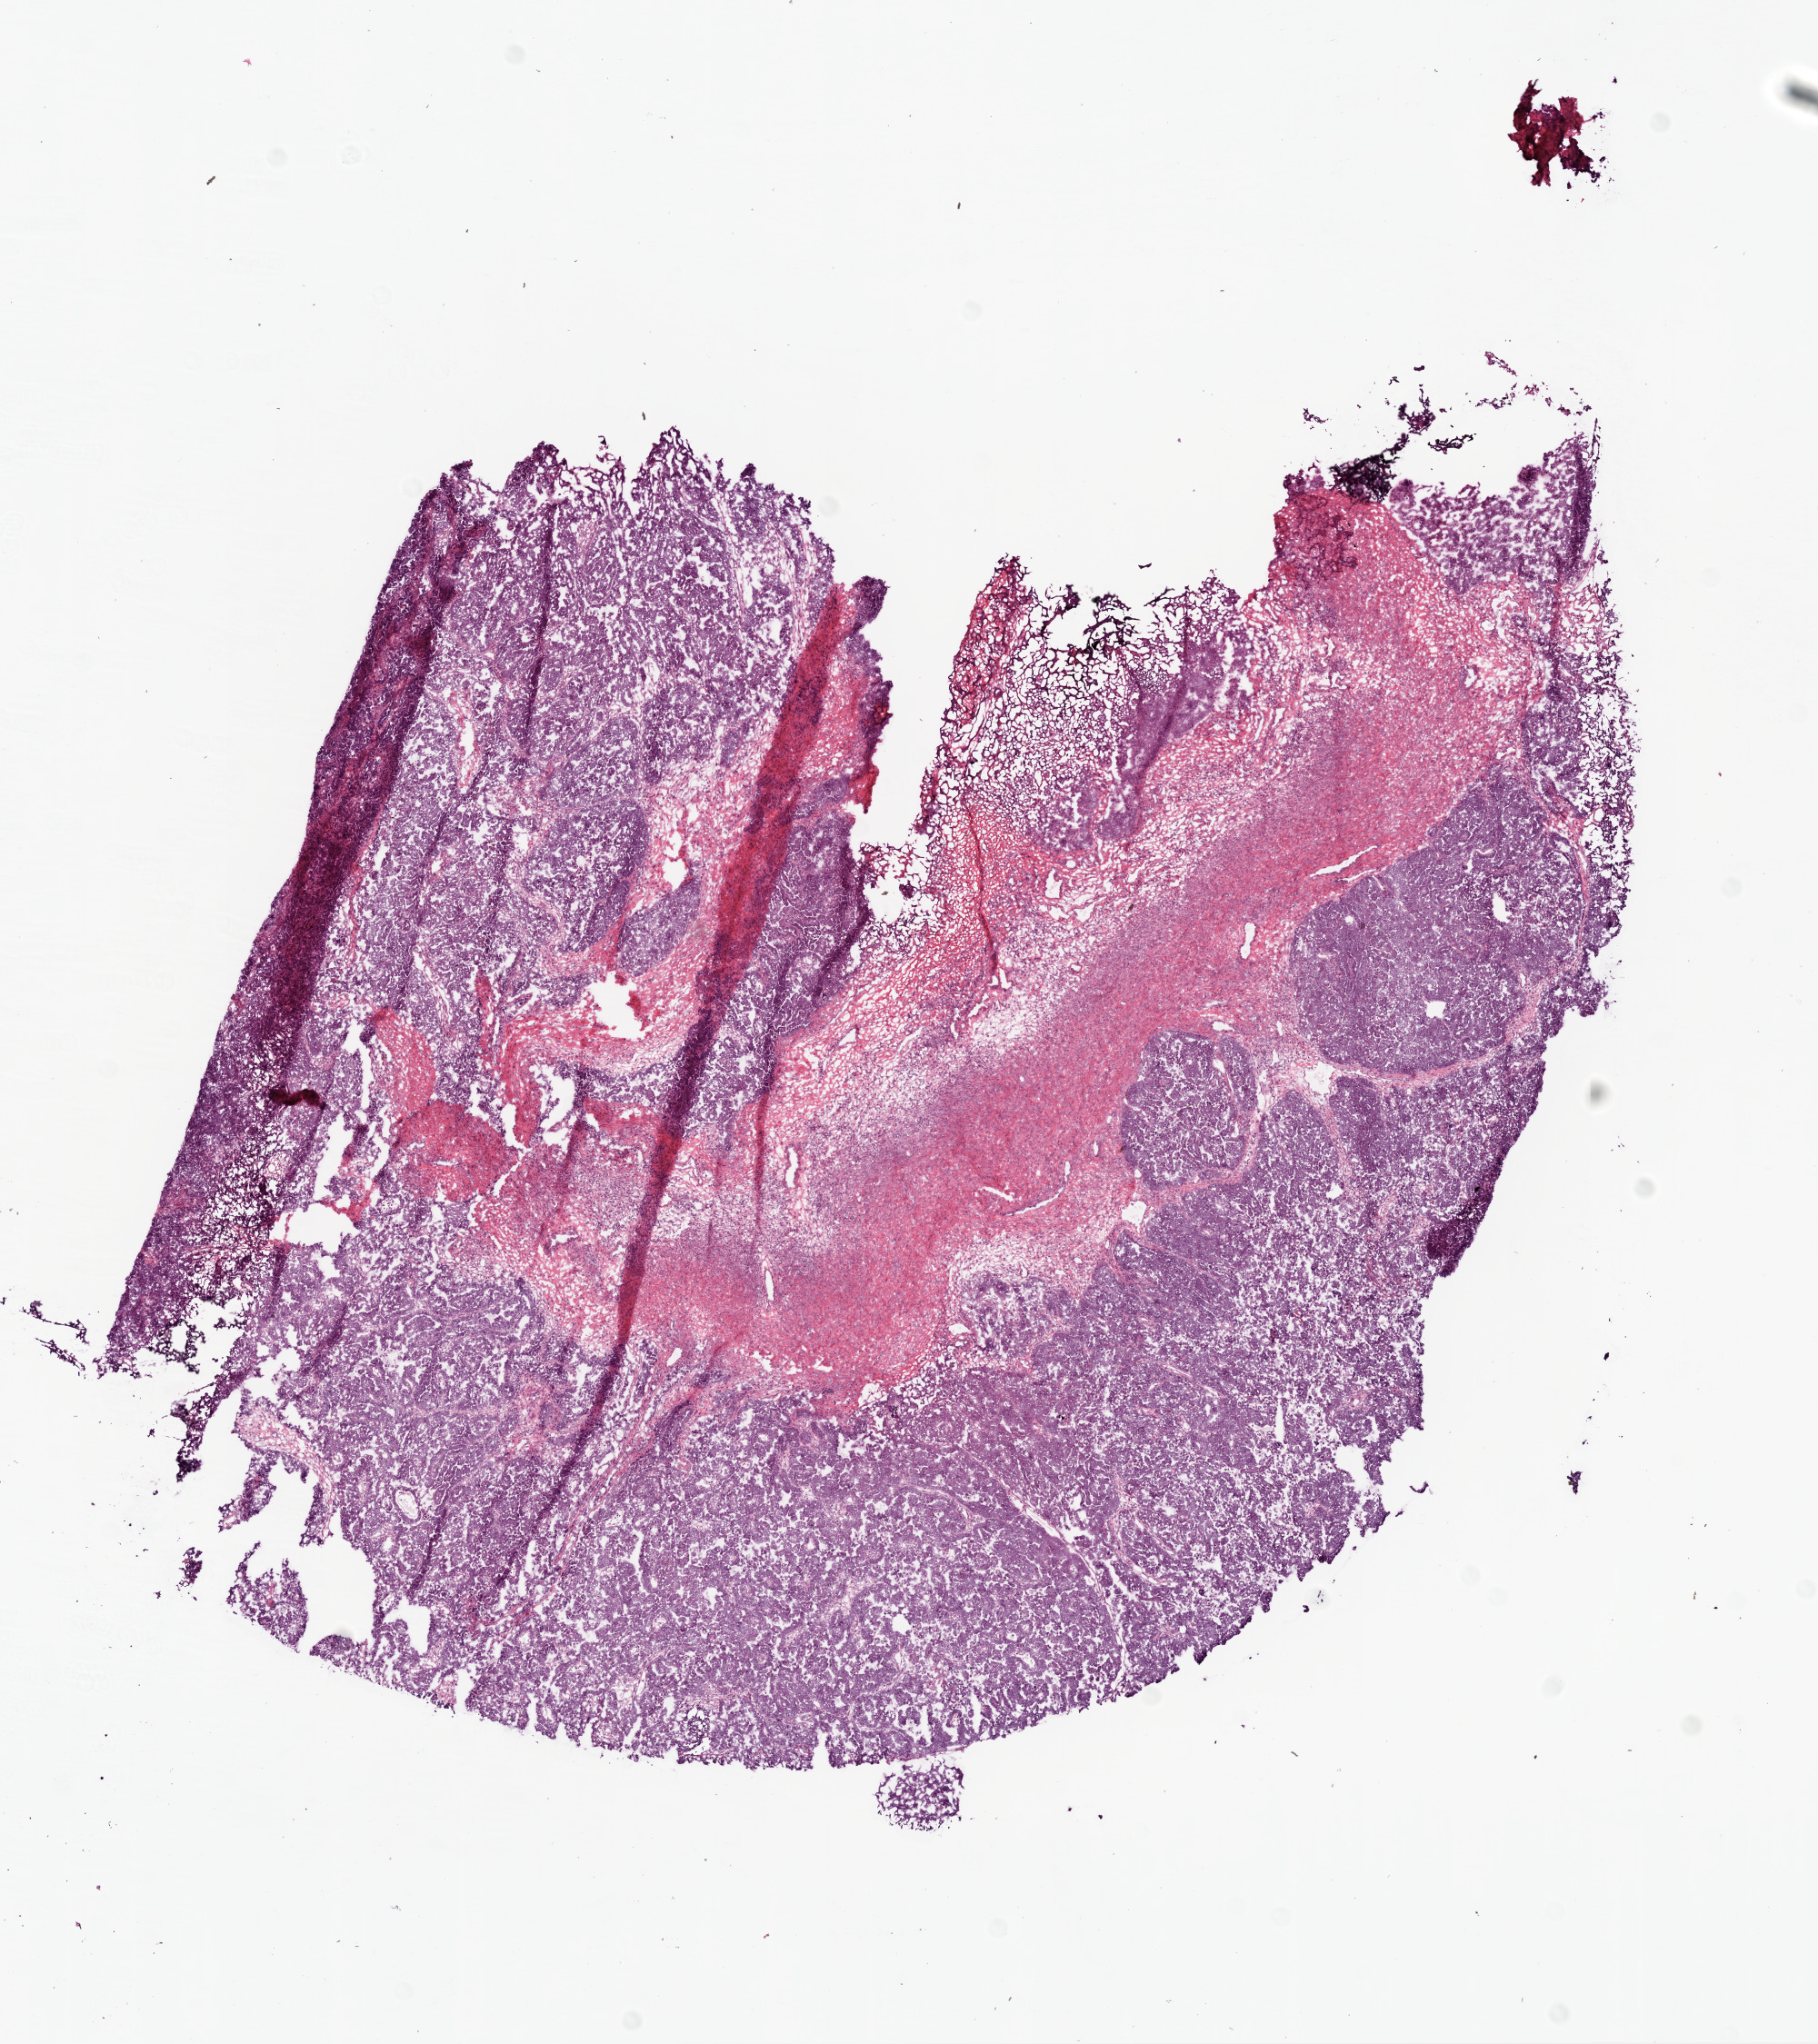
Digitized Hematoxylin and eosin (H&E) stained tissue section (whole slide), a low-resolution overview of the entire scanned area, about 8.0 x 9.0 mm (from a 20x scan), frozen section from the bottom of the tissue portion, primary tumour sample from the ovary. Patient: female, age at initial diagnosis 51 years. Histologic grade: G3 (poorly differentiated). Slide review estimates, as recorded: tumour cells 80%, tumour nuclei 85%, normal cells 17%, stromal cells 0%, necrosis 3%.
• pathologic diagnosis: Serous cystadenocarcinoma, NOS
• FIGO stage: IIIC